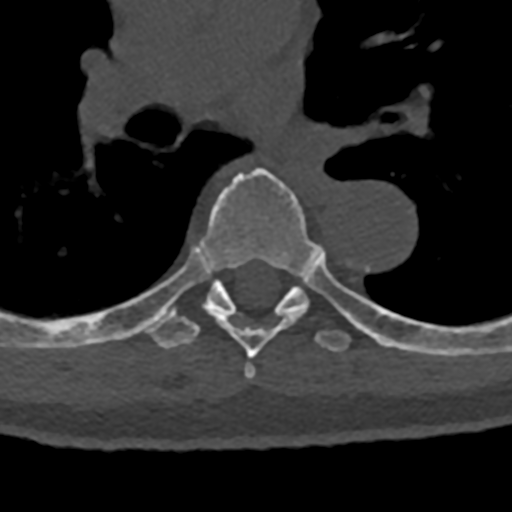
CT including the spine, one axial slice. Position 792 of 797 along the scan axis. Reconstruction kernel Br40s/3. Bone window (W 1800 / L 400 HU). 0.5 mm slice thickness. 512 × 512 image matrix, field of view 160 × 160 mm. Patient: male, 74 years. From the clinical record (not read from this slice): primary cancer: renal; vertebrae with lytic lesions (as recorded): T10, L1, L2, L3, L4, L5.
Annotated regions visible in this slice (semi-automatically segmented with operator editing):
- T6 vertebra: bounding box [x1, y1, x2, y2] px = [143, 167, 318, 380]
- T7 vertebra: [70, 245, 432, 355]